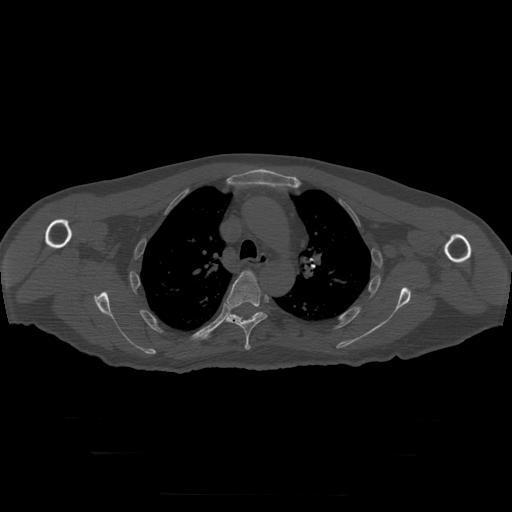
CT including the spine, one axial slice. Position 222 of 397 along the scan axis. Reconstruction kernel STANDARD. Bone window (W 1800 / L 400 HU). 1.25 mm slice thickness. 512 × 512 image matrix, field of view 510 × 510 mm. Patient age 73 years. From the clinical record (not read from this slice): primary cancer: prostate.
Structures marked on this image (semi-automatically segmented with operator editing):
- T5 vertebra: box from (x=226, y=271) to (x=268, y=351) px
- T6 vertebra: (x=229, y=312)–(x=261, y=320)